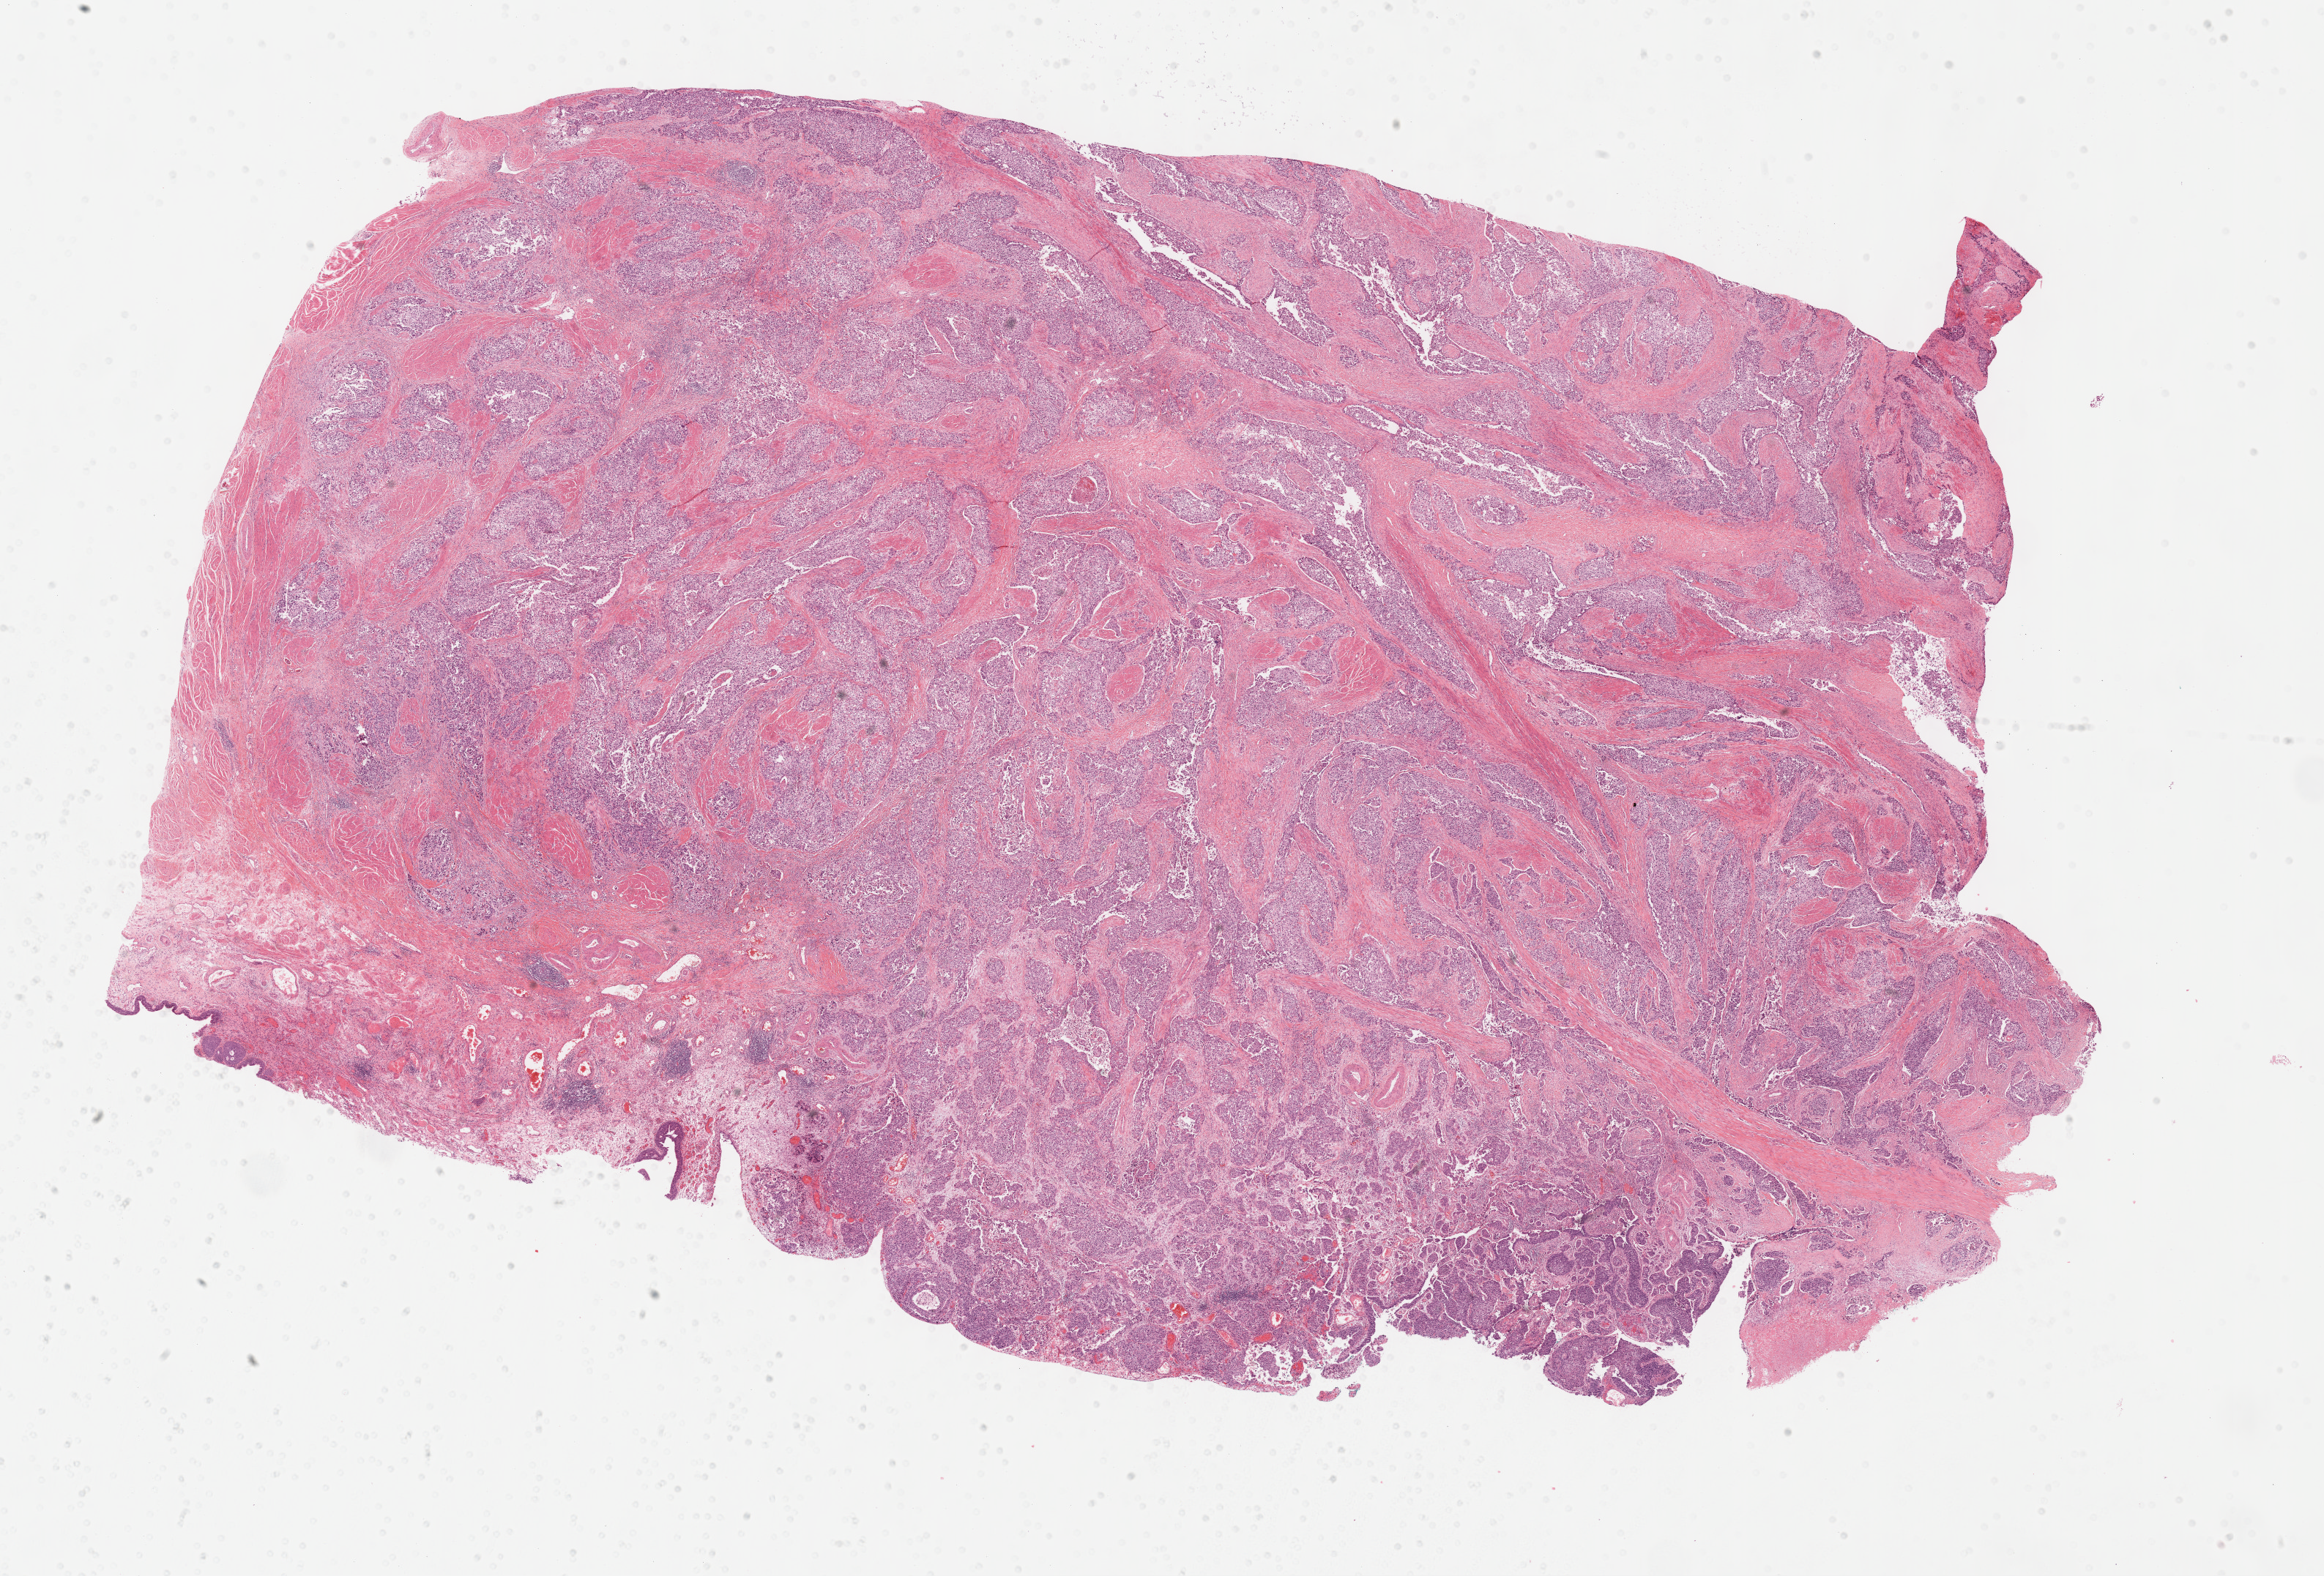
Digitized H&E-stained tissue section (whole slide), low-resolution overview of the scanned area, about 25.7 x 17.4 mm (acquisition: 40x scan); formalin-fixed paraffin-embedded (FFPE) diagnostic section; sample: primary tumour, bladder. Female patient; age at initial diagnosis 81 years. Histologic grade: high grade.
• AJCC pathologic stage: IV (6th edition)
• diagnosis: Transitional cell carcinoma